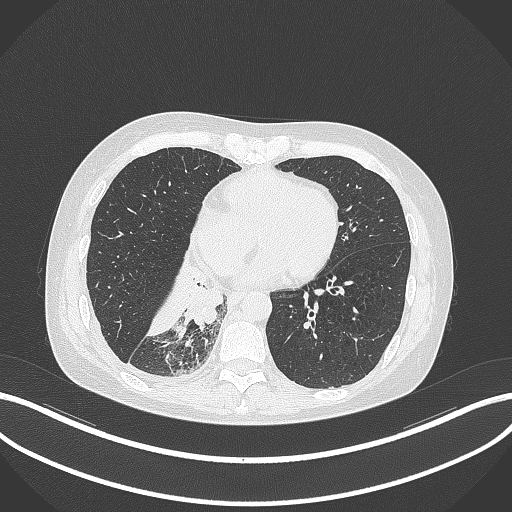
Chest CT, one axial slice. Slice 109 of 329 in the series (ordered by position). 120 kVp. Lung window (W 1500 / L -600 HU). 1 mm slice thickness. 512 × 512 image matrix. Patient: female, 63 years. Case-level facts recorded for this patient, not image findings: clinical TNM (as recorded): T1c N0 M0.
Annotated regions visible in this slice (rectangle marked by the reading radiologist):
- lung tumour (recorded histology: adenocarcinoma): bounding box [x1, y1, x2, y2] px = [177, 286, 223, 332]